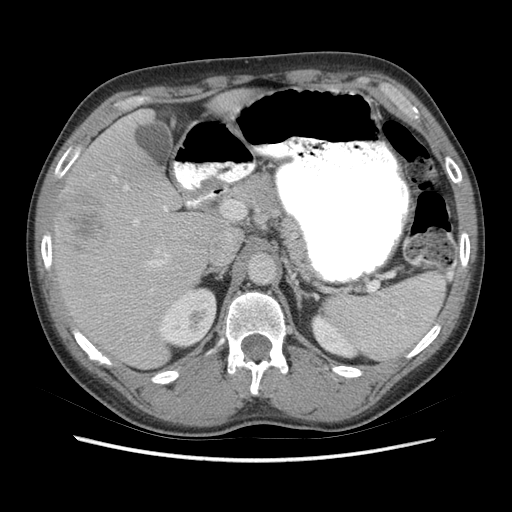
Contrast-enhanced abdominal CT (liver protocol), one axial slice. Slice 38 of 73 in the series (ordered by position). Reconstruction kernel STANDARD. 140 kVp. Soft-tissue window (W 400 / L 40 HU). 512 × 512 image matrix, field of view 360 × 360 mm. Case-level facts recorded for this patient, not image findings: diagnosis: hepatocellular carcinoma (patient treated with transarterial chemoembolisation; whether this scan precedes or follows treatment is not stated here); TNM stage (as recorded): Stage-IIIA; Child-Pugh class: A; tumour nodularity: multinodular; tumour size: 6.6 cm.
Annotated regions visible in this slice (semi-automatically segmented with operator editing):
- liver parenchyma outside the tumour (the mass and vessels are separate outlines, so this box may not span the whole liver): bounding box (x1, y1, x2, y2) in pixels: (52, 88, 254, 368)
- mass: (58, 192, 110, 256)
- liver vessels: (114, 178, 231, 291)